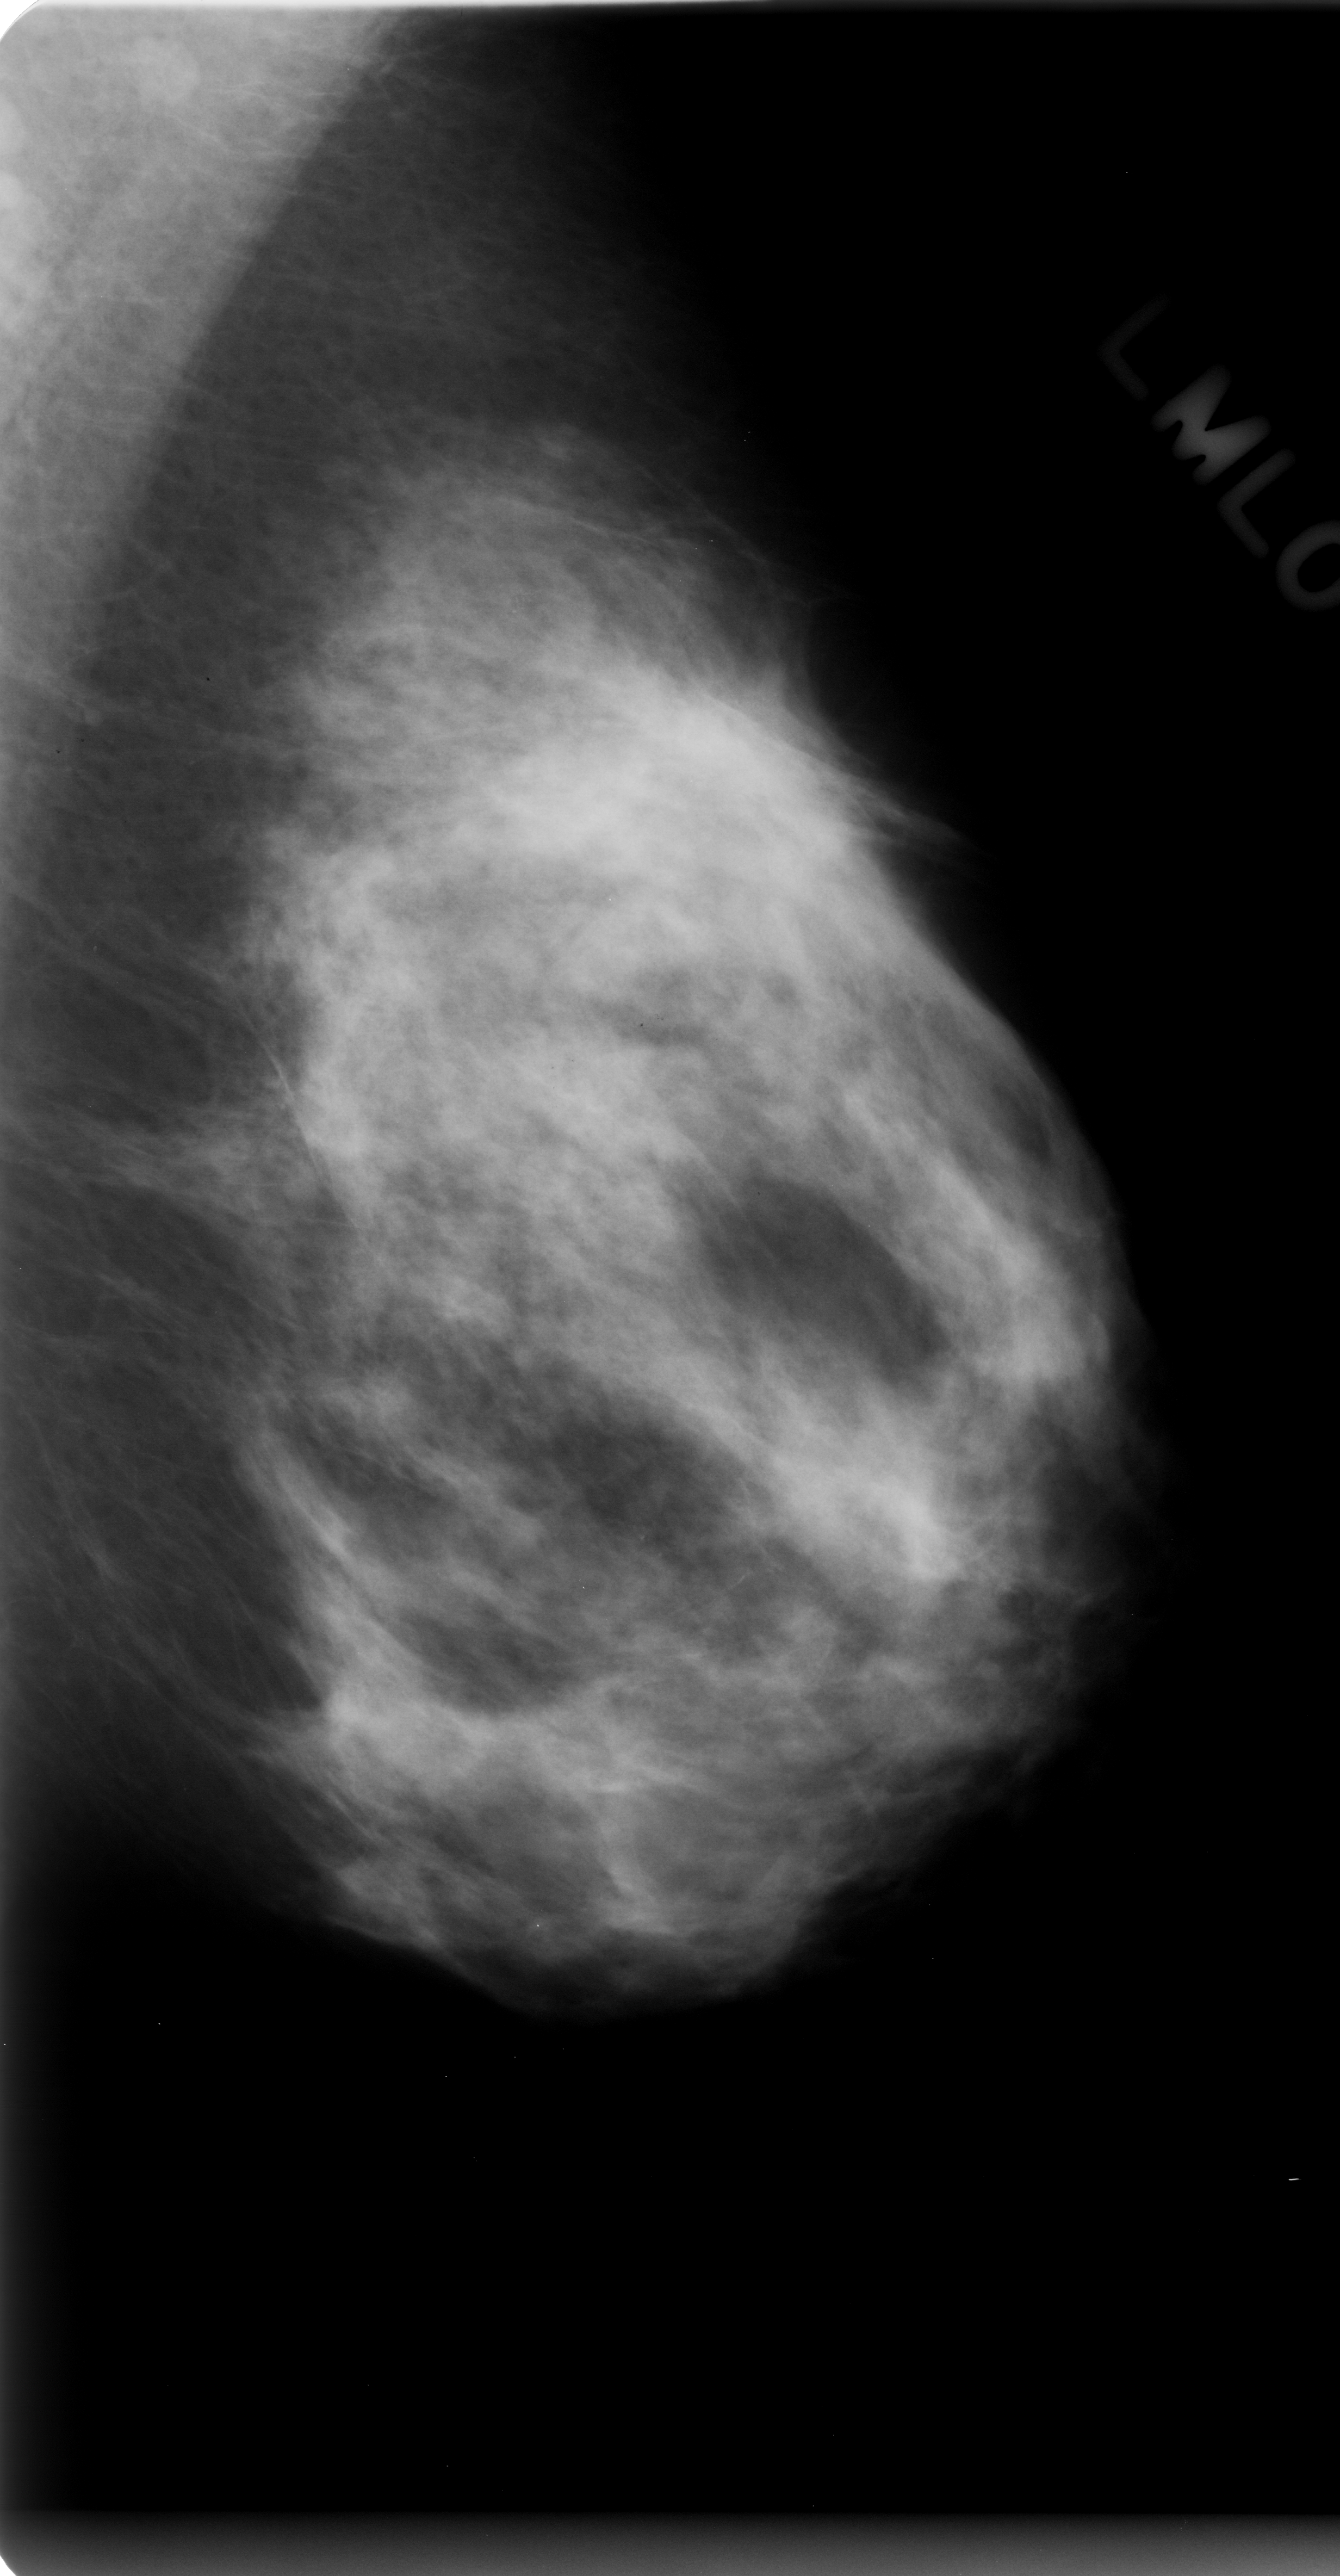
Digitized screen-film mammogram, left breast, mediolateral oblique (MLO) view.
Marked findings (only marked abnormalities are described; nothing is implied about the rest of the image): Finding 1 of 2: calcifications, morphology amorphous, distribution clustered; BI-RADS assessment category 4; subtlety rating 1 on a 1 (subtle) to 5 (obvious) scale; pathology result (as recorded, not read from the image): benign. Finding 2 of 2: calcifications, morphology amorphous, distribution clustered; BI-RADS assessment category 4; pathology result (as recorded, not read from the image): malignant.